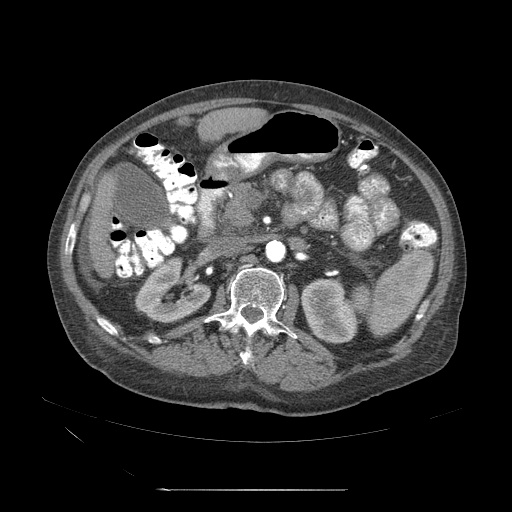
Contrast-enhanced abdominal CT (liver protocol), one axial slice. Slice 14 of 71 in the series (ordered by position). 120 kVp. Soft-tissue window (W 400 / L 40 HU). 2.5 mm slice thickness. 512 × 512 image matrix. Case-level facts recorded for this patient, not image findings: diagnosis: hepatocellular carcinoma (patient treated with transarterial chemoembolisation; whether this scan precedes or follows treatment is not stated here); TNM stage (as recorded): Stage-II; Child-Pugh class: A; tumour size: 1 cm.
Outlined on this slice (semi-automatic segmentation, software-assisted and operator-edited):
- abdominal aorta: bounding box [x1, y1, x2, y2] px = [265, 242, 286, 264]